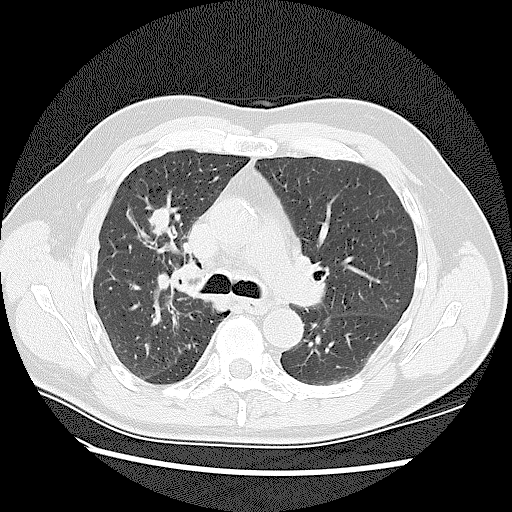
Low-dose screening chest CT, axial slice. First (baseline) screen. Lung window (W 1500 / L -600 HU). 2.5 mm slice thickness. Lung (sharp) reconstruction kernel (LUNG). Slice 49 of 128 in the series. 512 × 512 image matrix. Male, age 72 years at enrolment.
Expert-annotated lung lesion, bounding box <133,199,180,238> (left, top, right, bottom; pixels). The screening reader recorded 2 non-calcified nodules or masses ≥4 mm on this exam; which of them this box marks is not recorded. Official screen result: positive, change unspecified: nodule(s) >= 4 mm or enlarging nodule(s), mass(es), or other non-specific abnormalities suspicious for lung cancer. Participant outcome: lung cancer diagnosed 42 days after this screen — adenocarcinoma, NOS, right upper lobe, stage IV (AJCC 6th edition), 45 mm at pathology.